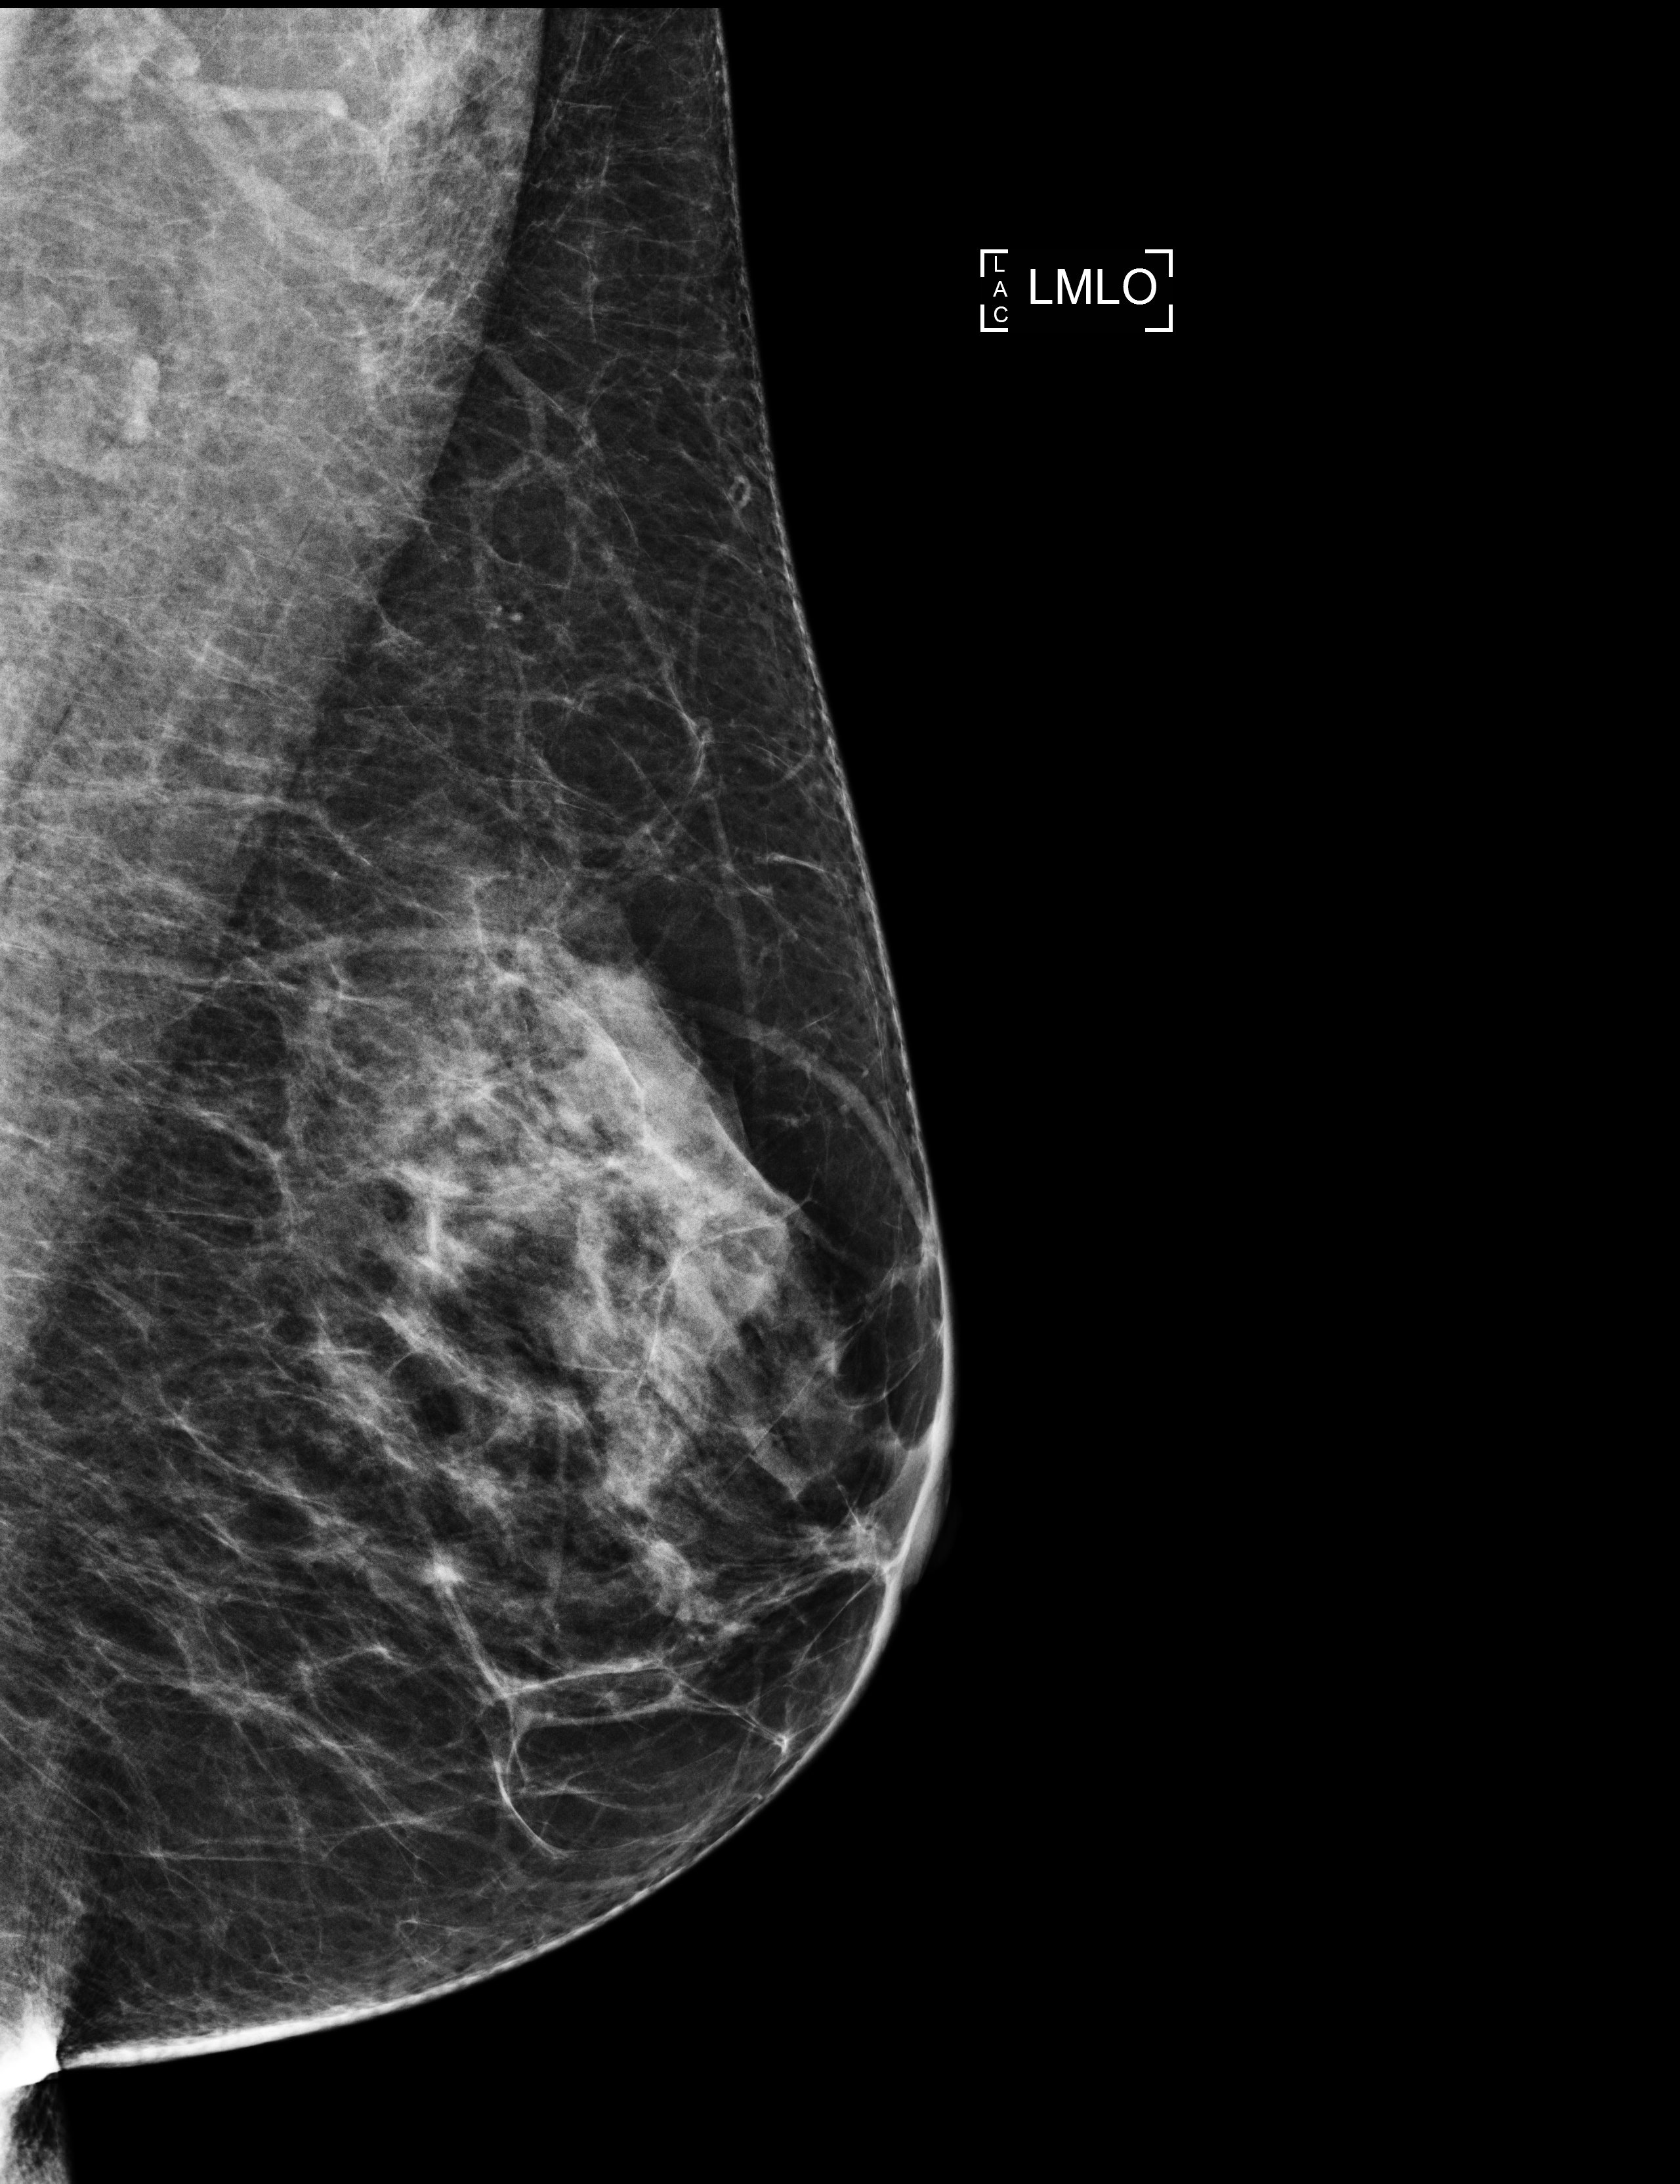
Digital mammogram (FFDM), left breast, mediolateral oblique (MLO) view, annual screening mammography examination. Patient: female, 63 years.
- breast density at the screening exam (both breasts): heterogeneously dense (BI-RADS density category c)
- final BI-RADS assessment for this screening round (tomosynthesis exam, both breasts): category 1
- recall: recalled for additional imaging after this screen